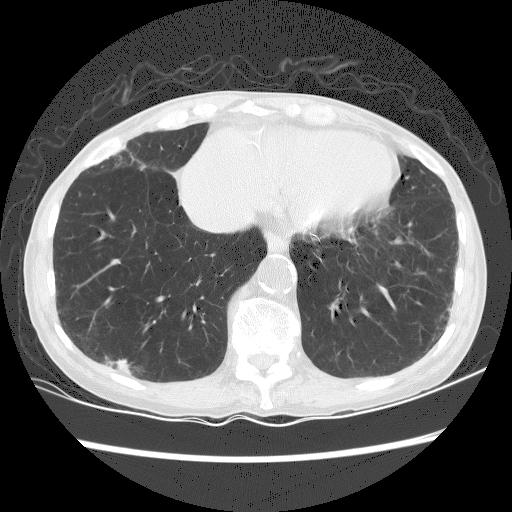
Low-dose screening chest CT, one axial slice. Slice 56 of 156 in the series (ordered by position). 120 kVp. Lung window (W 1500 / L -600 HU). 512 × 512 image matrix, field of view 320 × 320 mm.
Annotated regions visible in this slice (expert manual segmentation):
- lesion 1 (tumor, lower lobe of right lung): bounding box (x1, y1, x2, y2) in pixels: (105, 356, 132, 374)